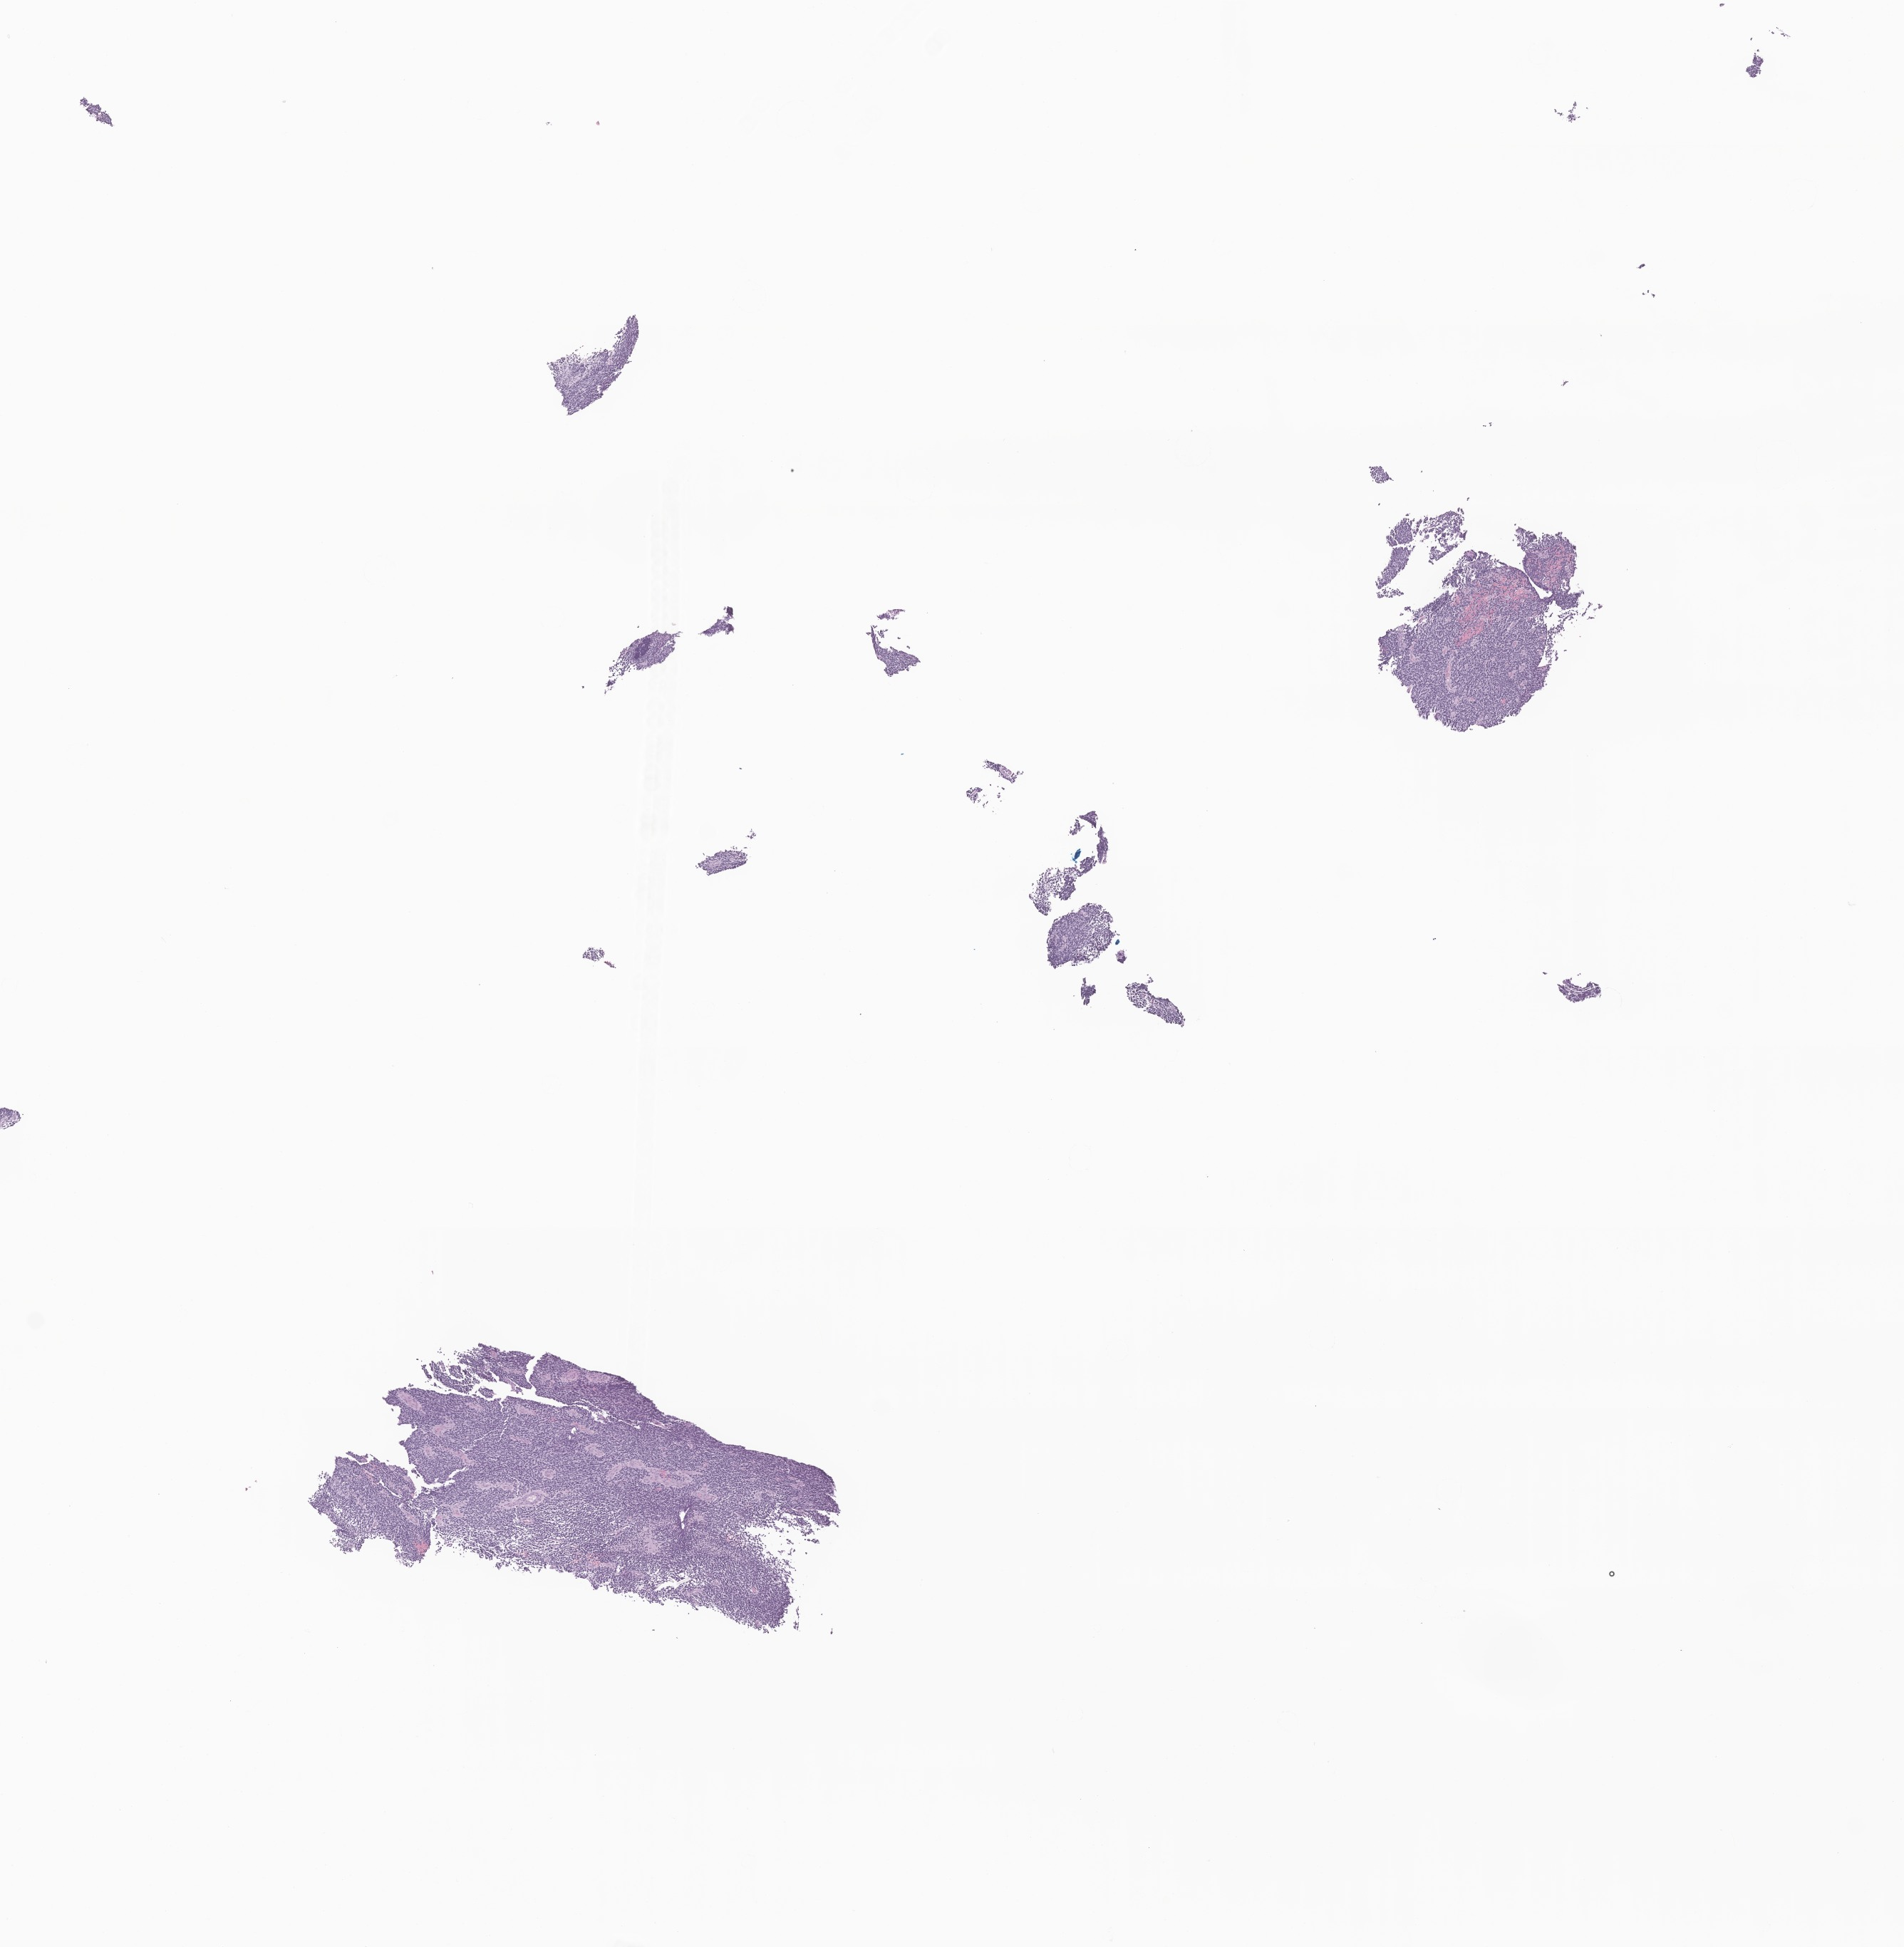
Digitized haematoxylin and eosin-stained section of tumor tissue from the brain — a low-resolution overview of the entire scanned area, about 11.3 x 11.5 mm; formalin-fixed, paraffin-embedded (FFPE) tissue. Patient male; age 171 months (14 years 3 months).
Recorded diagnosis: Neoplasm, malignant.